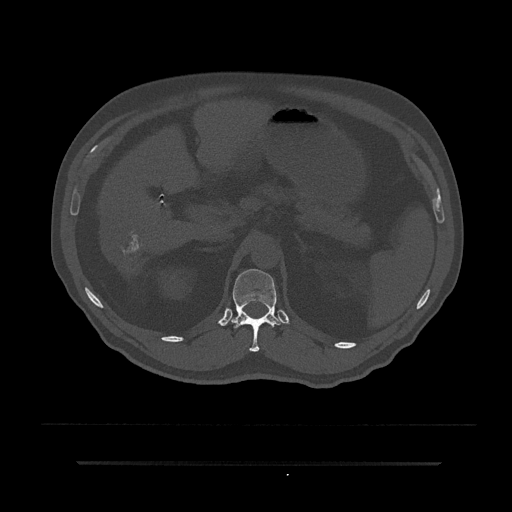
CT including the spine, one axial slice. Reconstruction kernel Br40s/3. 120 kVp. Bone window (W 1800 / L 400 HU). 512 × 512 image matrix, field of view 464 × 464 mm. Patient: male, 59 years. From the clinical record (not read from this slice): primary cancer: bile ducts; vertebrae with lytic lesions (as recorded): T10.
Structures marked on this image (semi-automatic segmentation, software-assisted and operator-edited):
- T12 vertebra: bounding box <231,269,282,352> (left, top, right, bottom; pixels)